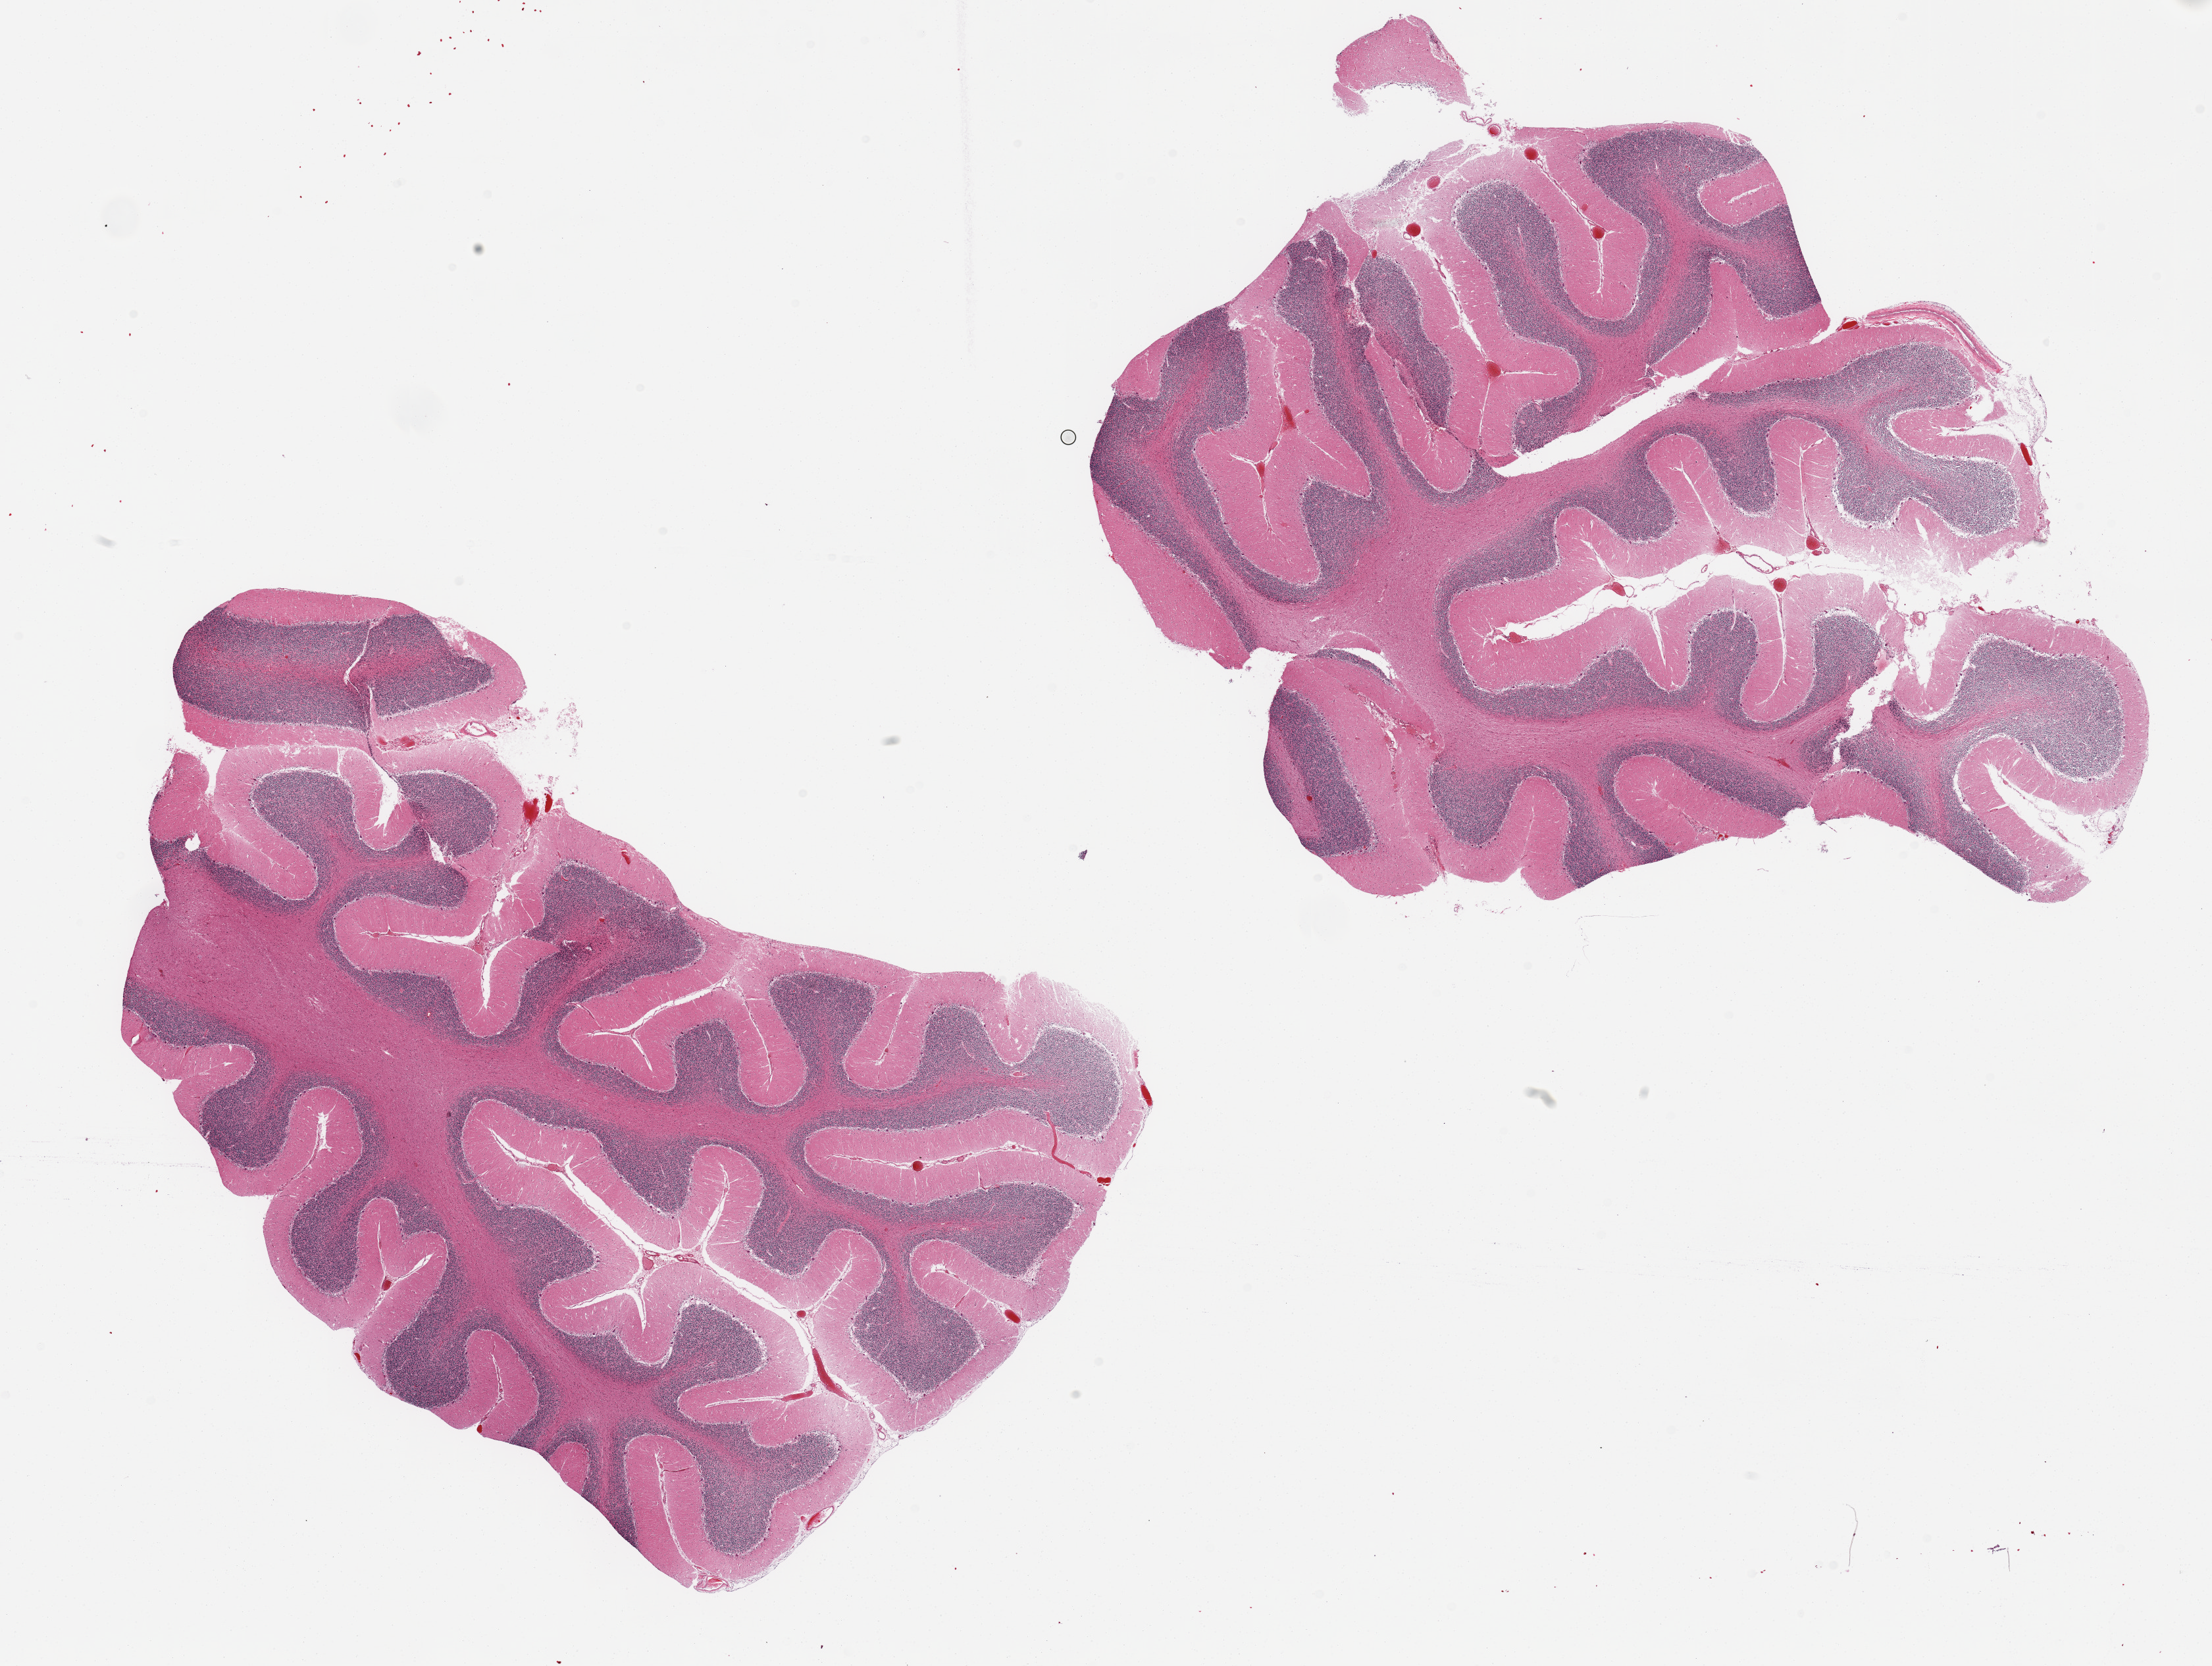
Whole-slide image, H&E stain, shown as a low-resolution overview of the whole scanned area (about 26.6 x 20.0 mm), PAXgene-fixed, paraffin-embedded tissue, section of cerebellum (target tissue), donor tissue sample.
• reviewer comment on this tissue sample: 2 pieces, Purkinje cells well visualized